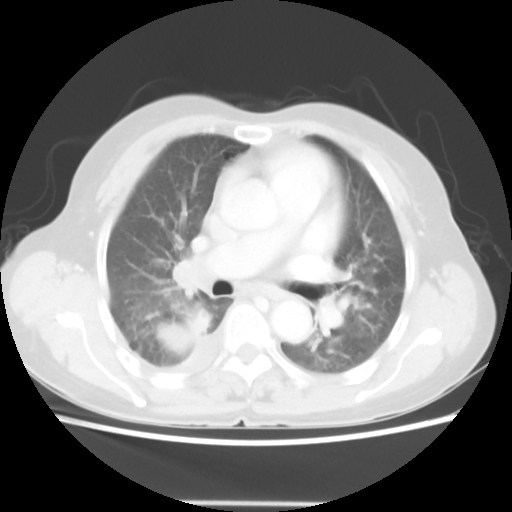
Chest CT, one axial slice. Position 30 of 52 along the scan axis. Reconstruction kernel STANDARD. 140 kVp. Lung window (W 1500 / L -600 HU). 5 mm slice thickness. 512 × 512 image matrix, field of view 337 × 337 mm. Patient: female, 67 years. From the clinical record (not read from this slice): clinical TNM (as recorded): T3 N1 M1.
Annotated regions visible in this slice (bounding box drawn by a radiologist):
- lung tumour (recorded histology: adenocarcinoma): box from (x=152, y=304) to (x=213, y=362) px